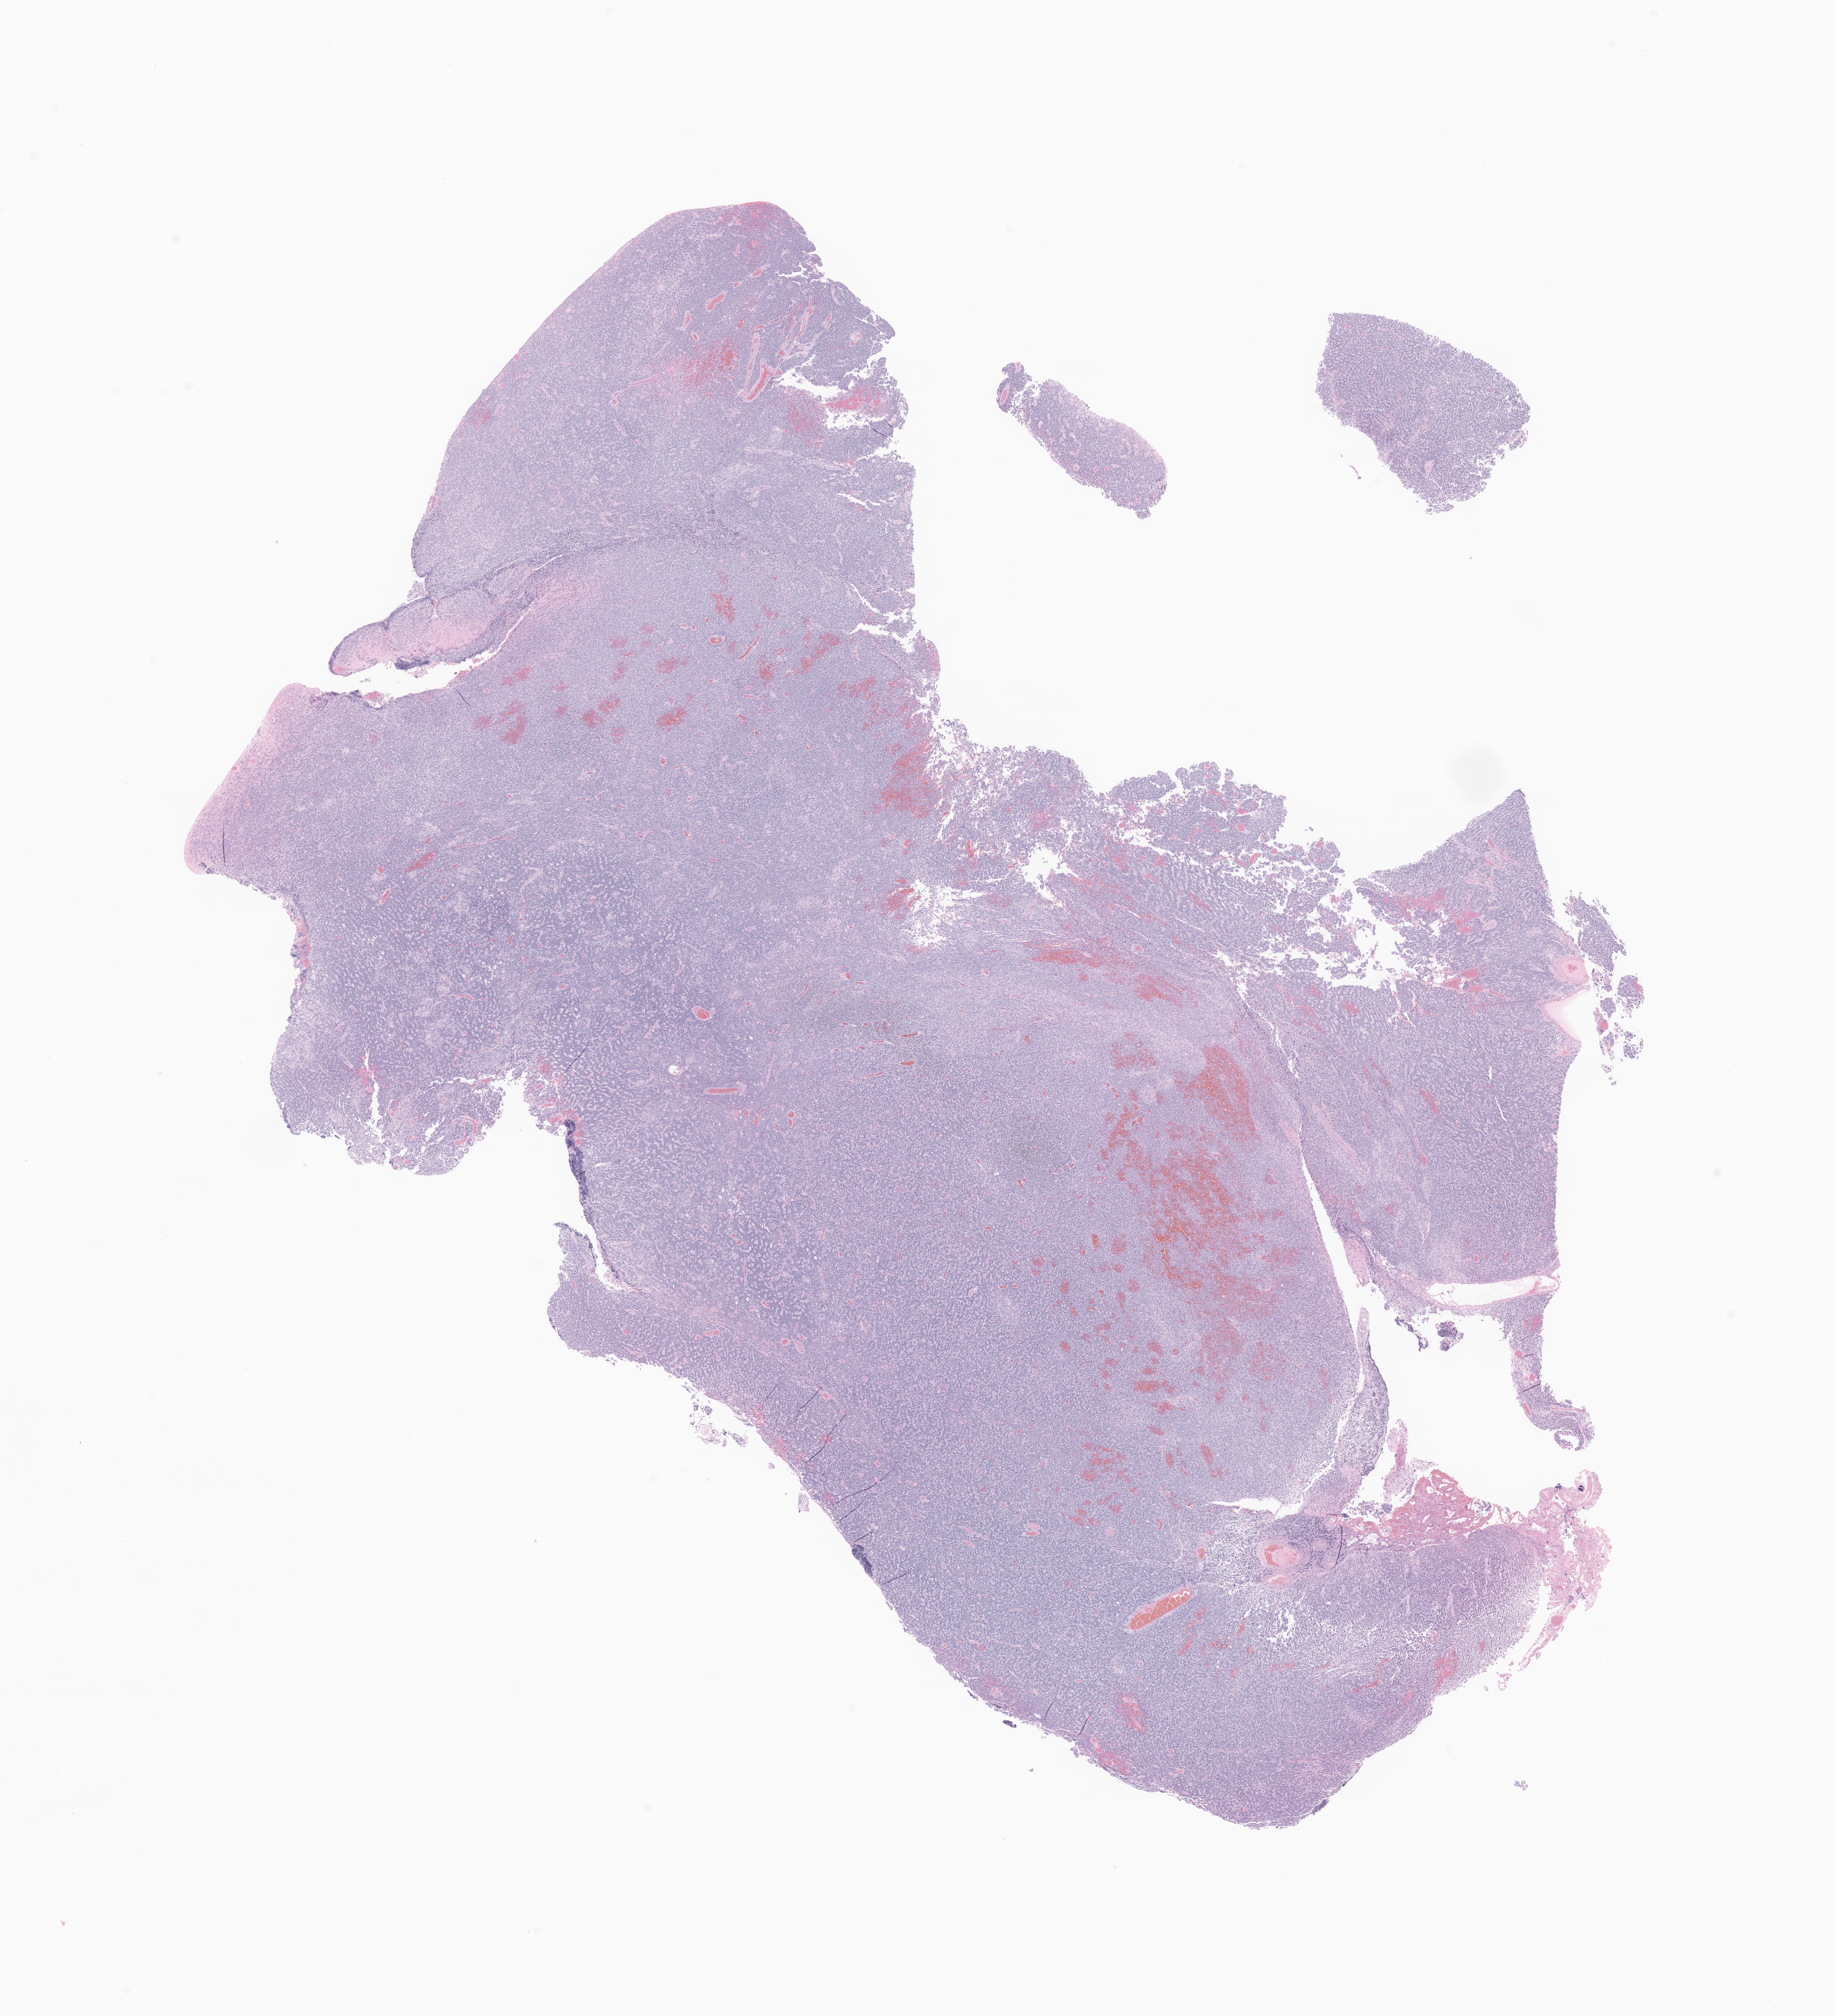
Hematoxylin and eosin (H&E) whole-slide image of tumor tissue from the cerebellum — whole scanned area (about 17.6 x 19.3 mm) shown as a low-resolution overview, formalin-fixed, paraffin-embedded (FFPE) tissue. Patient: male, age 88 months (7 years 4 months).
Diagnosis (ICD-O-3 morphology term): Medulloblastoma, NOS.